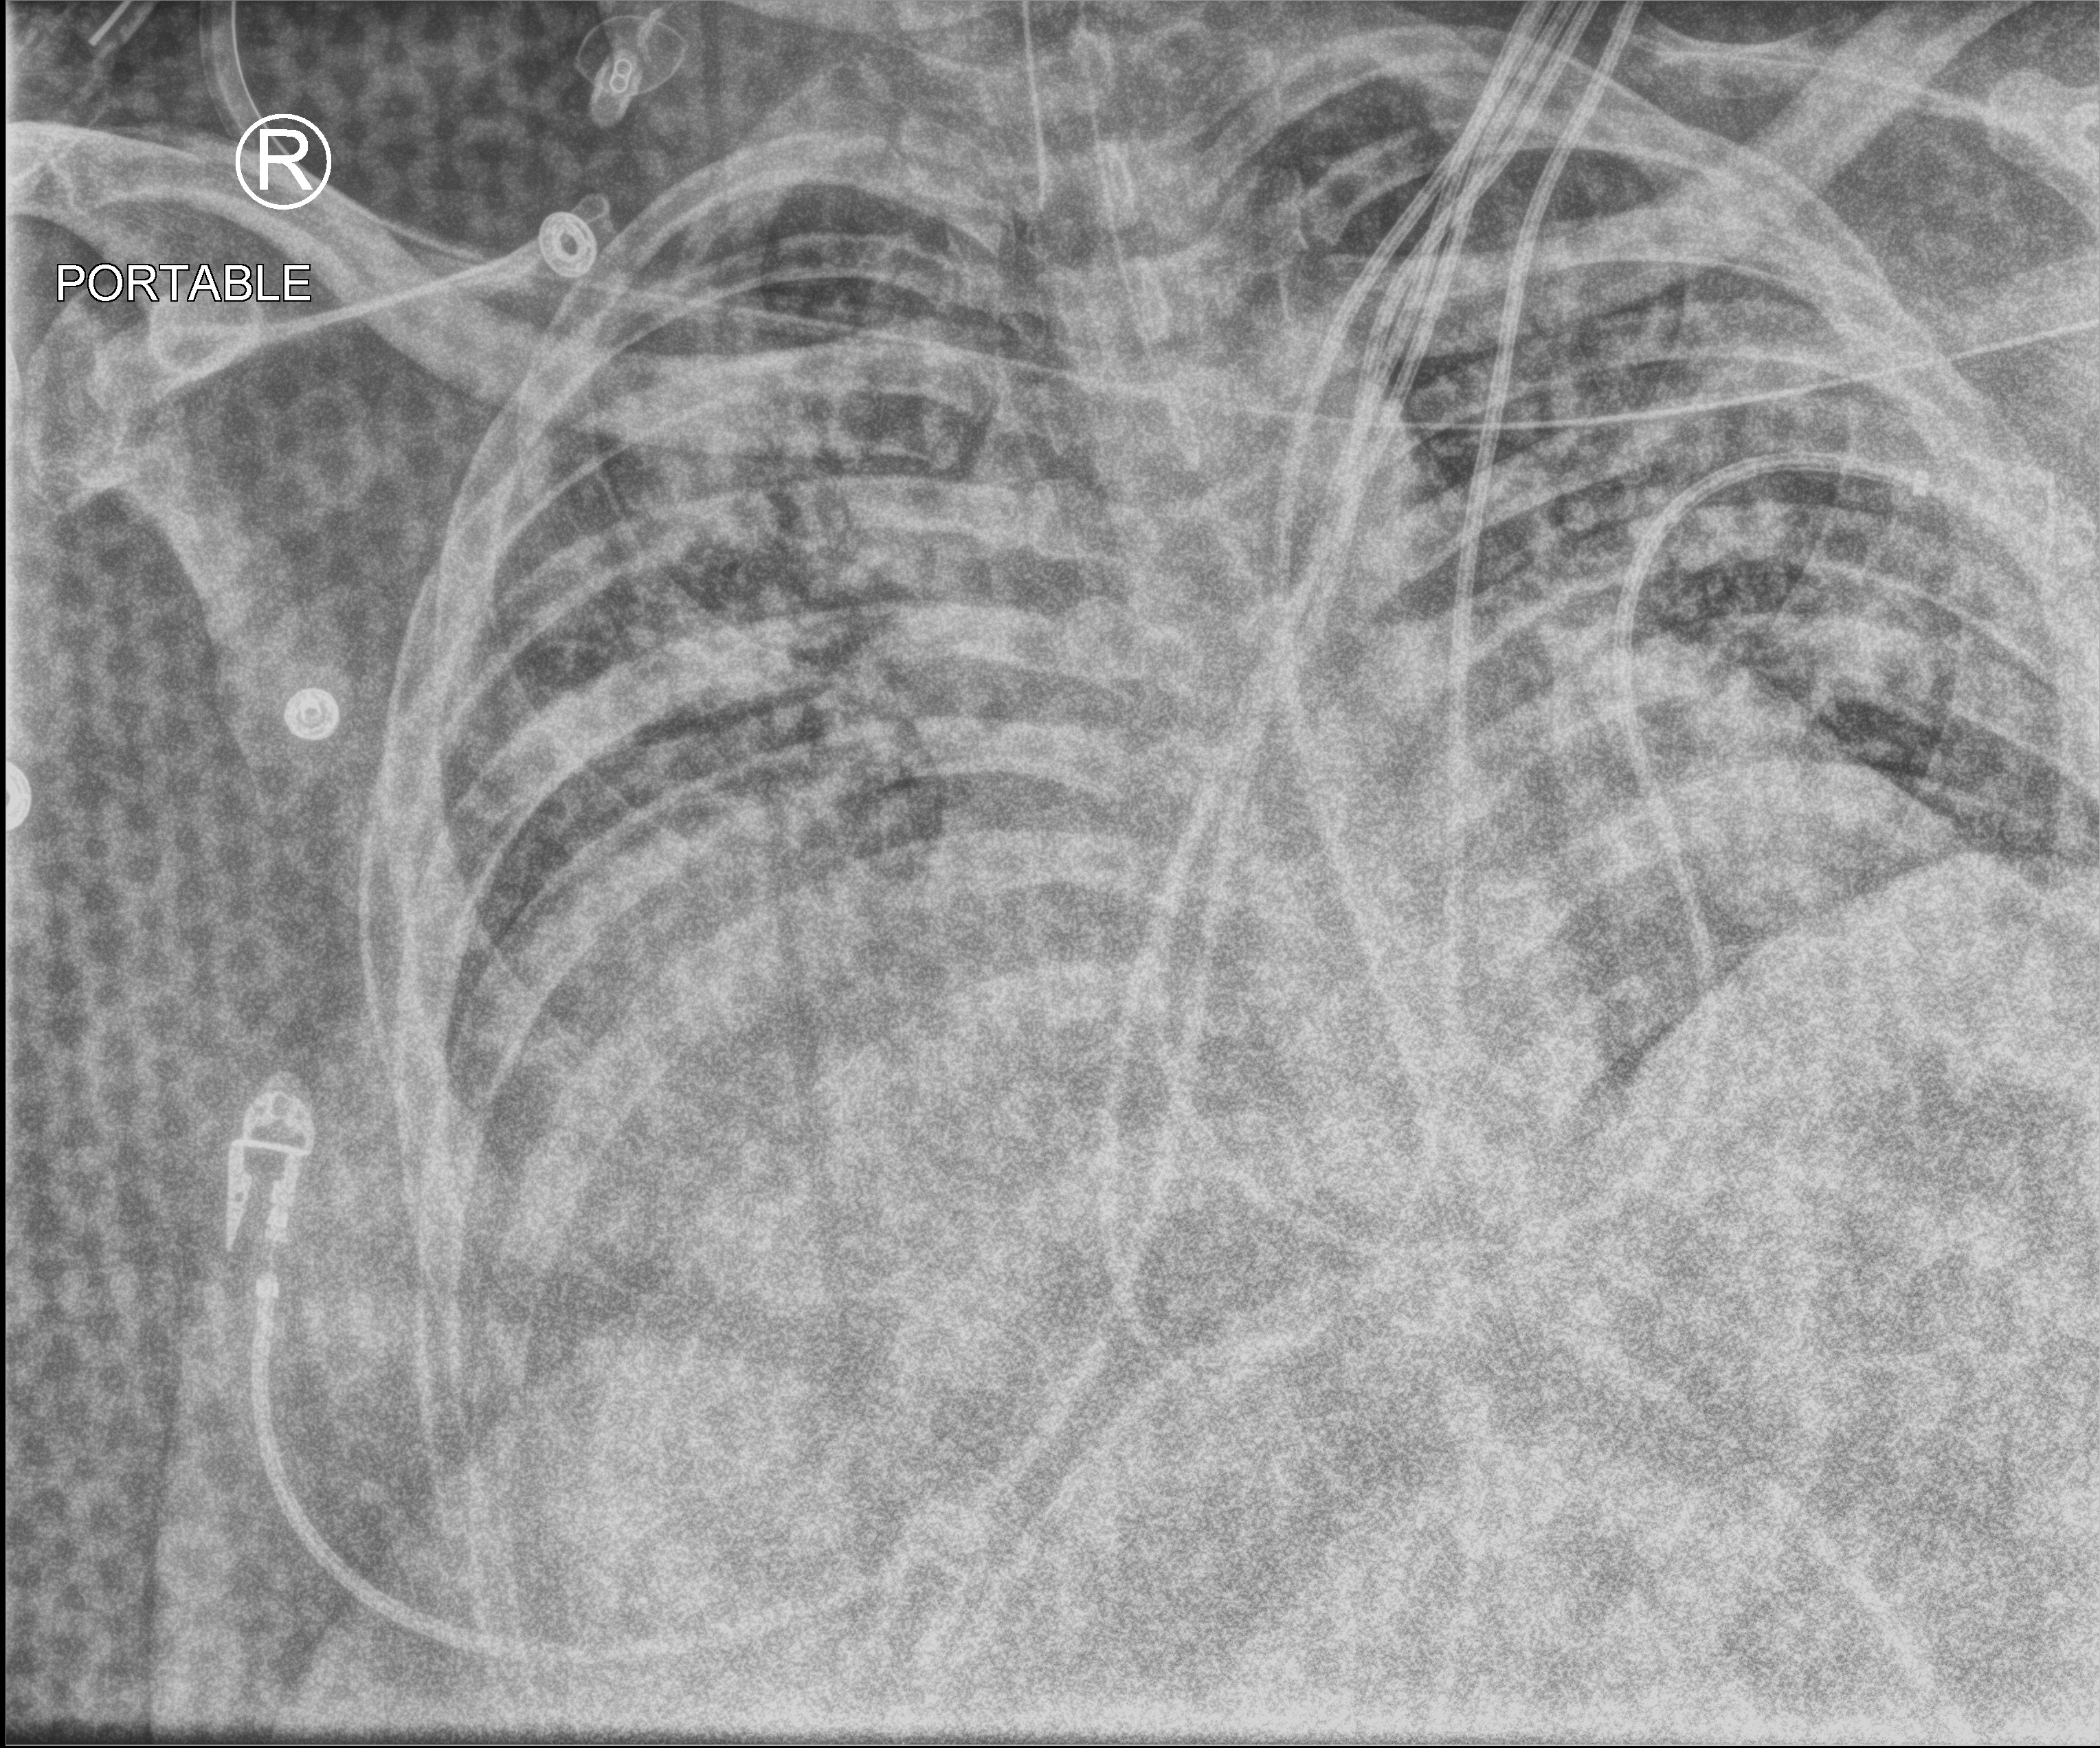
Bedside chest radiograph (computed radiography), anteroposterior (AP) projection. Patient hospitalised with COVID-19; male, aged 18–59 years.
Hospital-stay facts (about this admission, not read from this image; timing relative to this image not recorded):
- chronic kidney disease (admission record): no
- mechanically ventilated during this hospital stay: yes